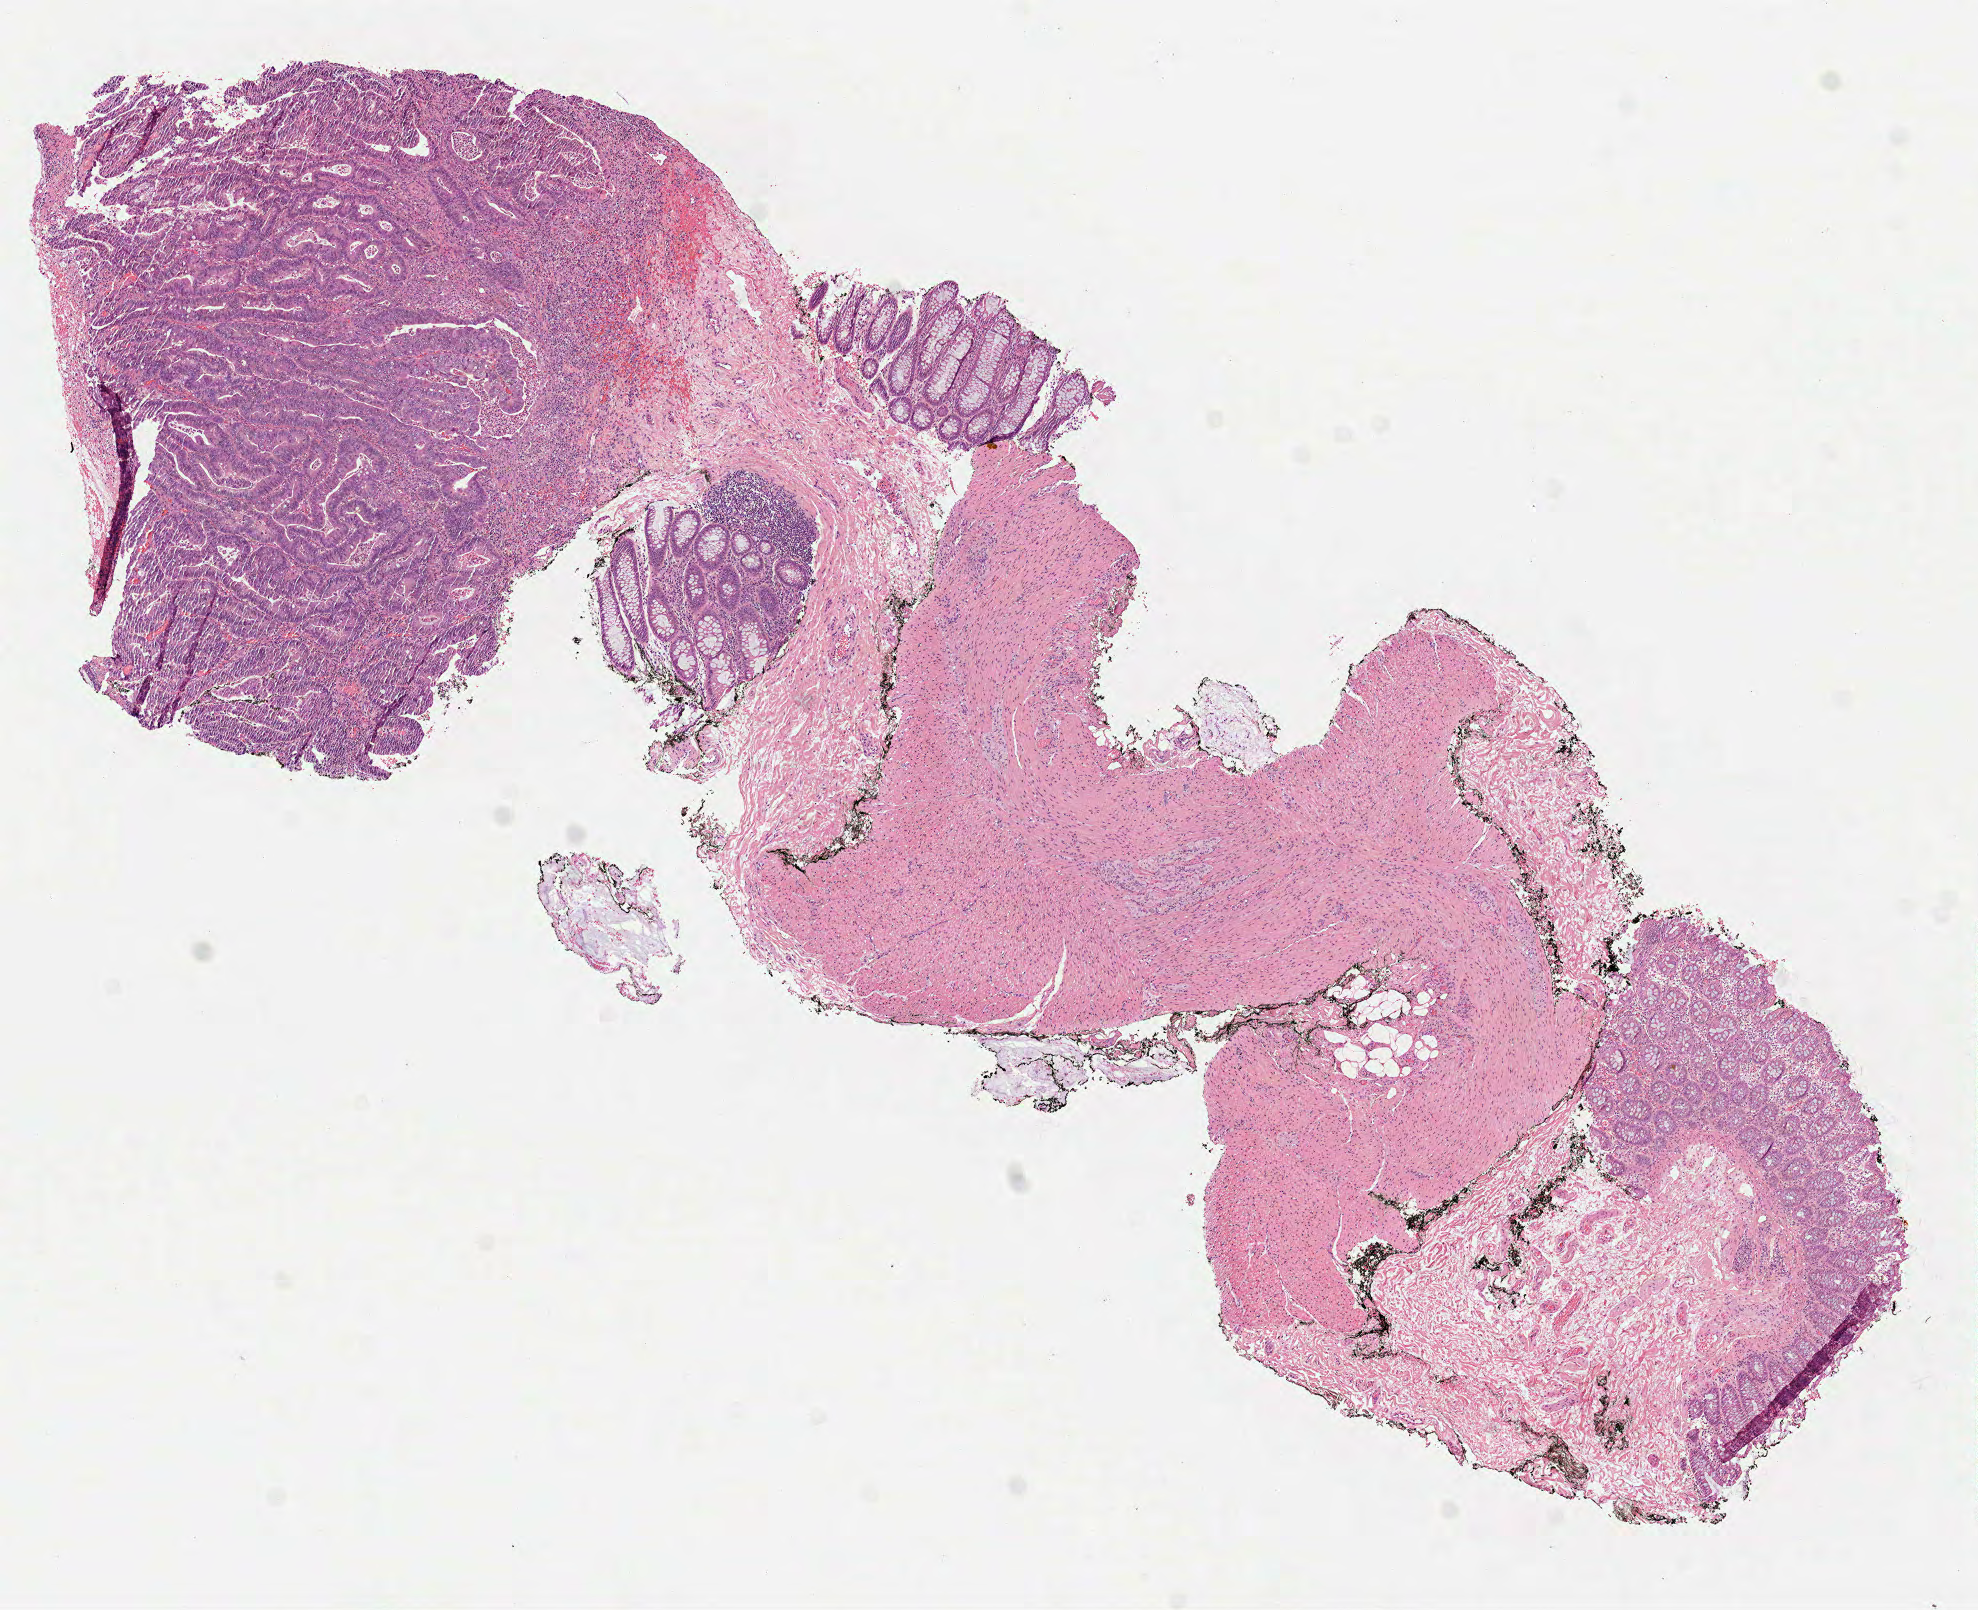
Hematoxylin and eosin (H&E) stained whole-slide image, whole scanned area (about 8.0 x 6.5 mm) shown as a low-resolution overview; formalin-fixed paraffin-embedded (FFPE) diagnostic section; sample: primary tumour, colon. Male, age 58 years at initial diagnosis.
* lymph nodes positive (case pathology): 0 of 12 examined
* histologic diagnosis: Adenocarcinoma, NOS (ascending colon)